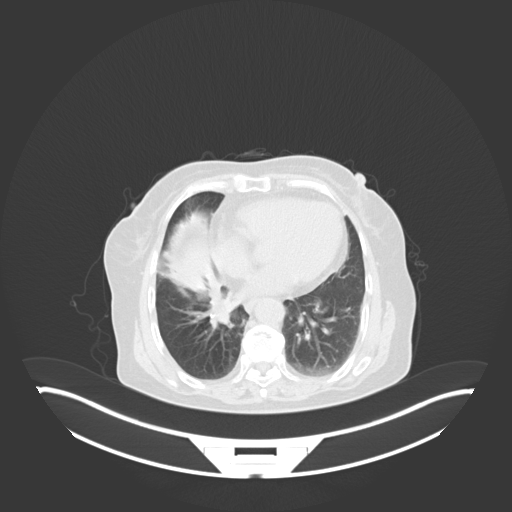
Chest CT, one axial slice. Position 17 of 76 along the scan axis. 120 kVp. Lung window (W 1500 / L -600 HU). 512 × 512 image matrix. Patient: female, 75 years. From the clinical record (not read from this slice): clinical TNM (as recorded): T1b N0 M1a; histopathological grade: G1.
Outlined on this slice (bounding box drawn by a radiologist):
- lung tumour (recorded histology: squamous cell carcinoma): bounding box <204,295,237,329> (left, top, right, bottom; pixels)